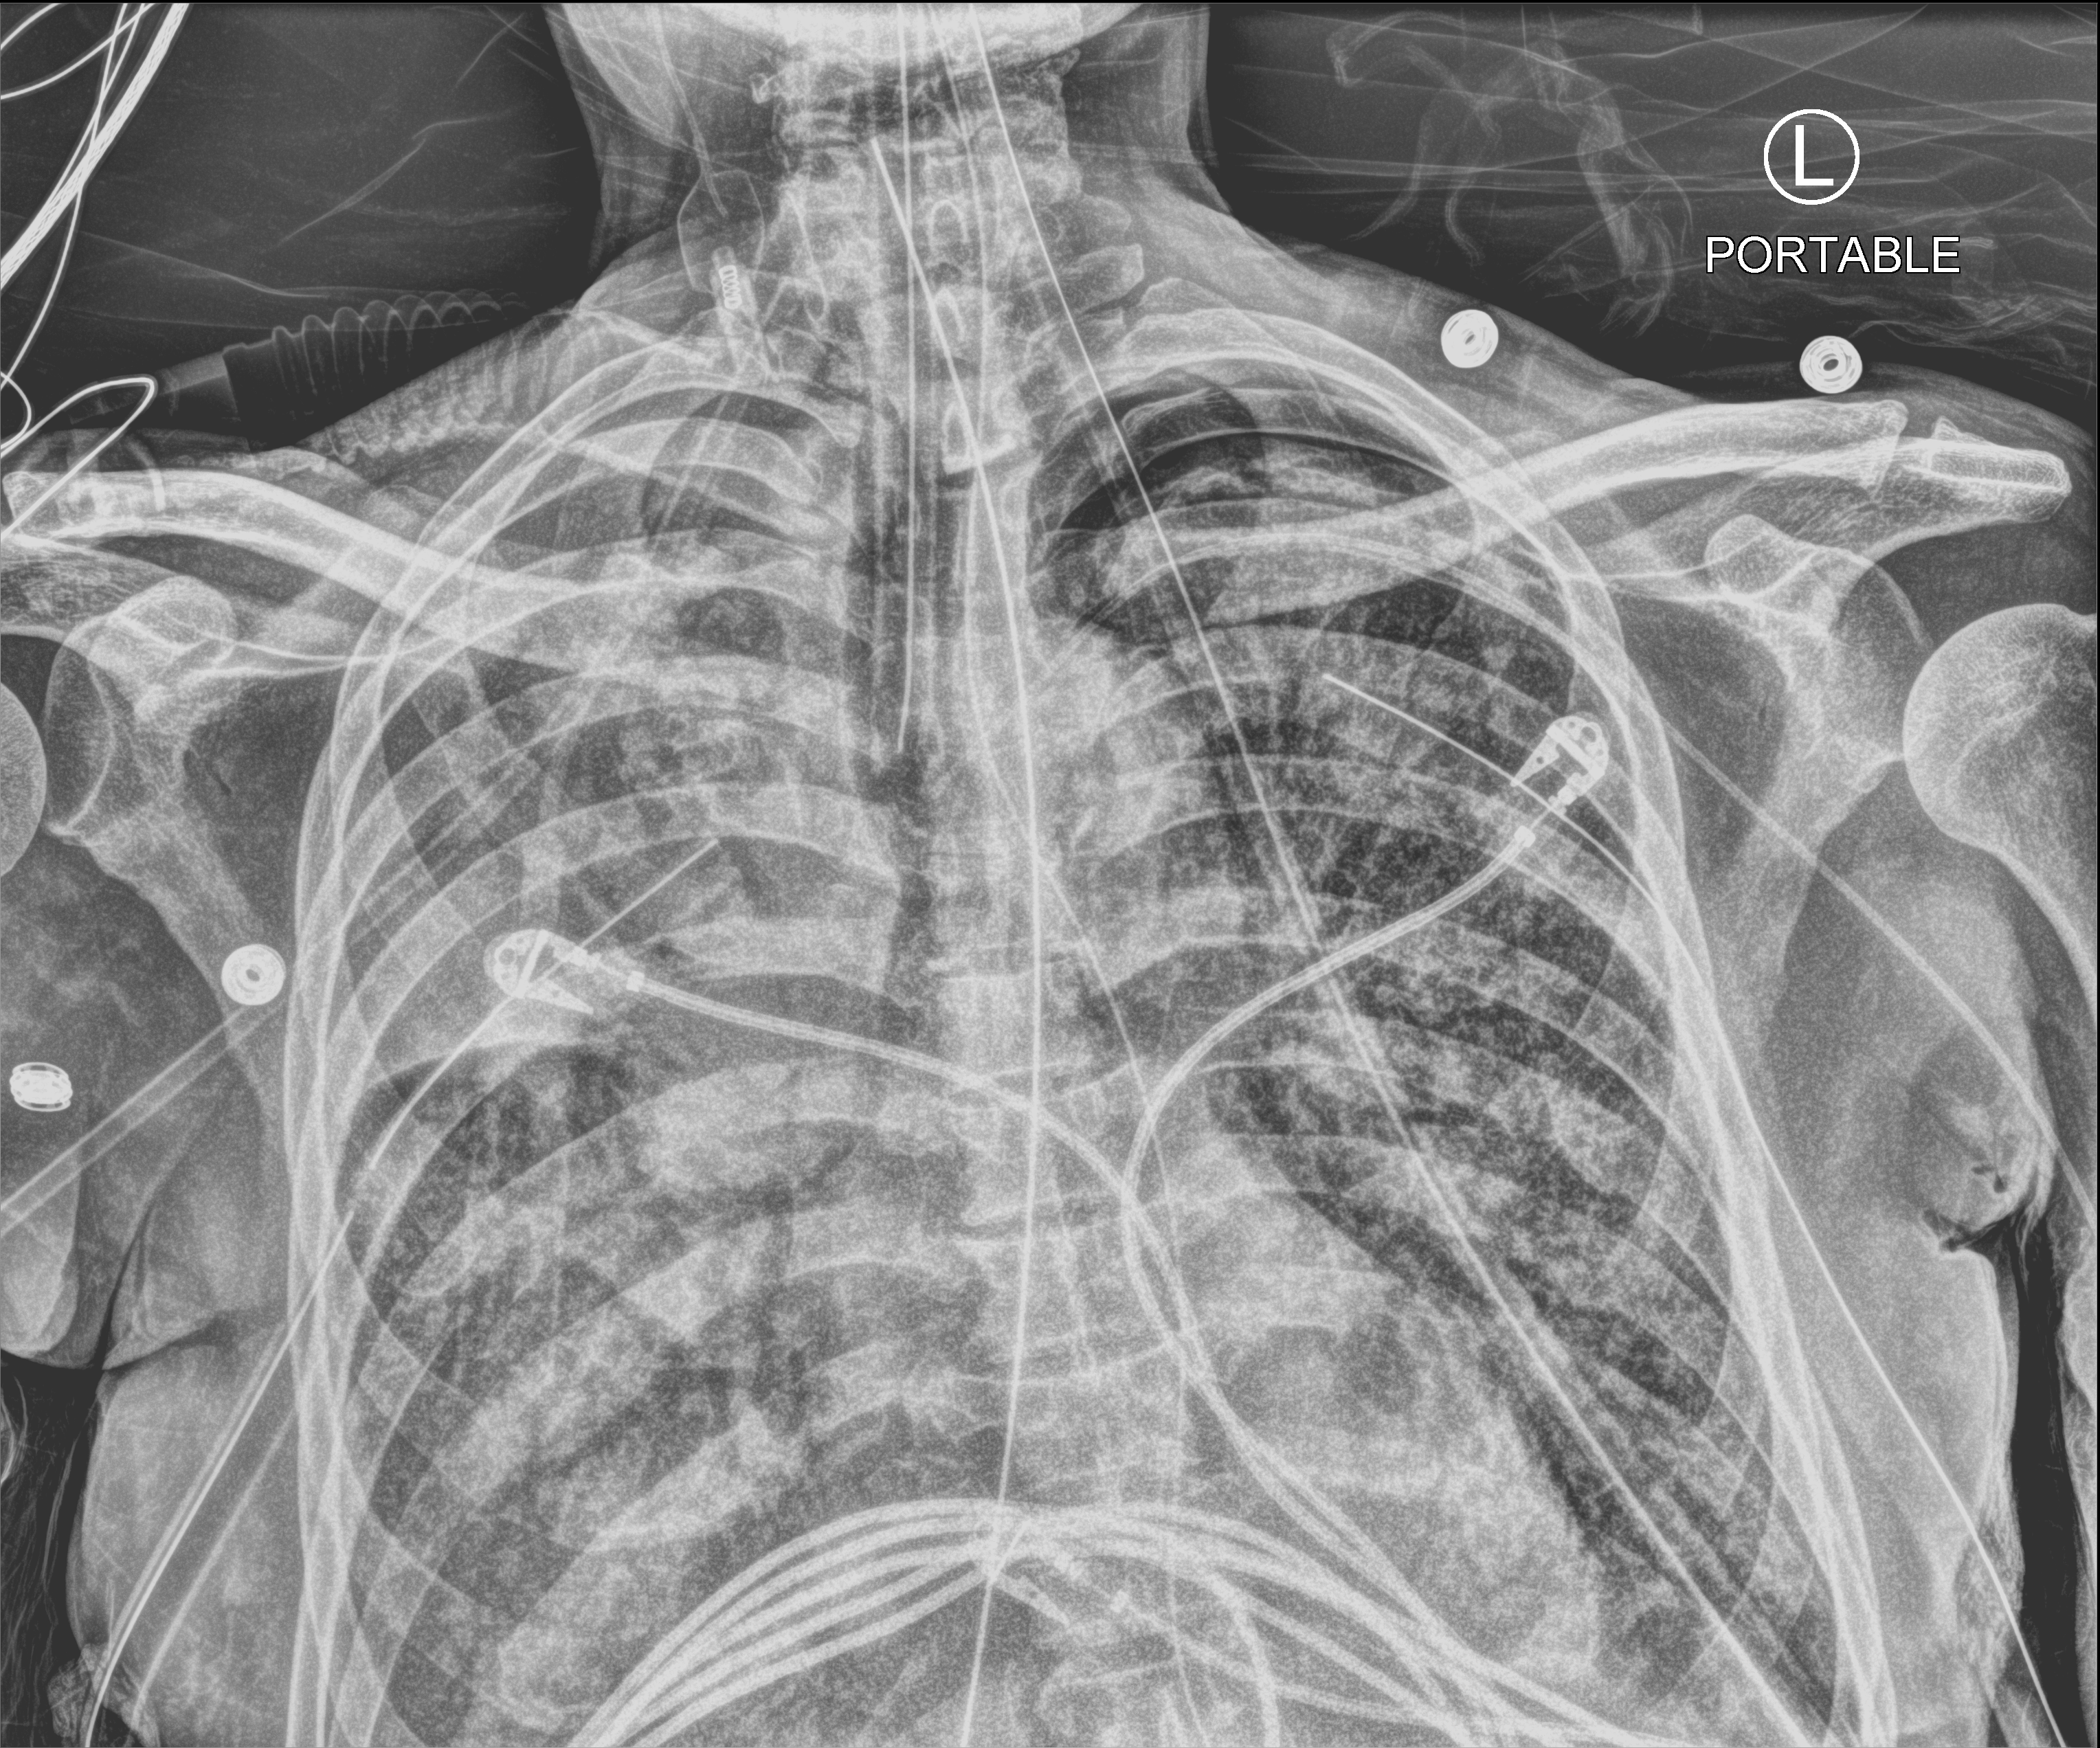
Chest X-ray (portable), anteroposterior (AP) projection. Patient hospitalised with COVID-19; male, aged 60–74 years.
From the hospital-stay record, not from the radiograph (when in the stay this image was taken is not recorded): mechanically ventilated during this hospital stay: yes.